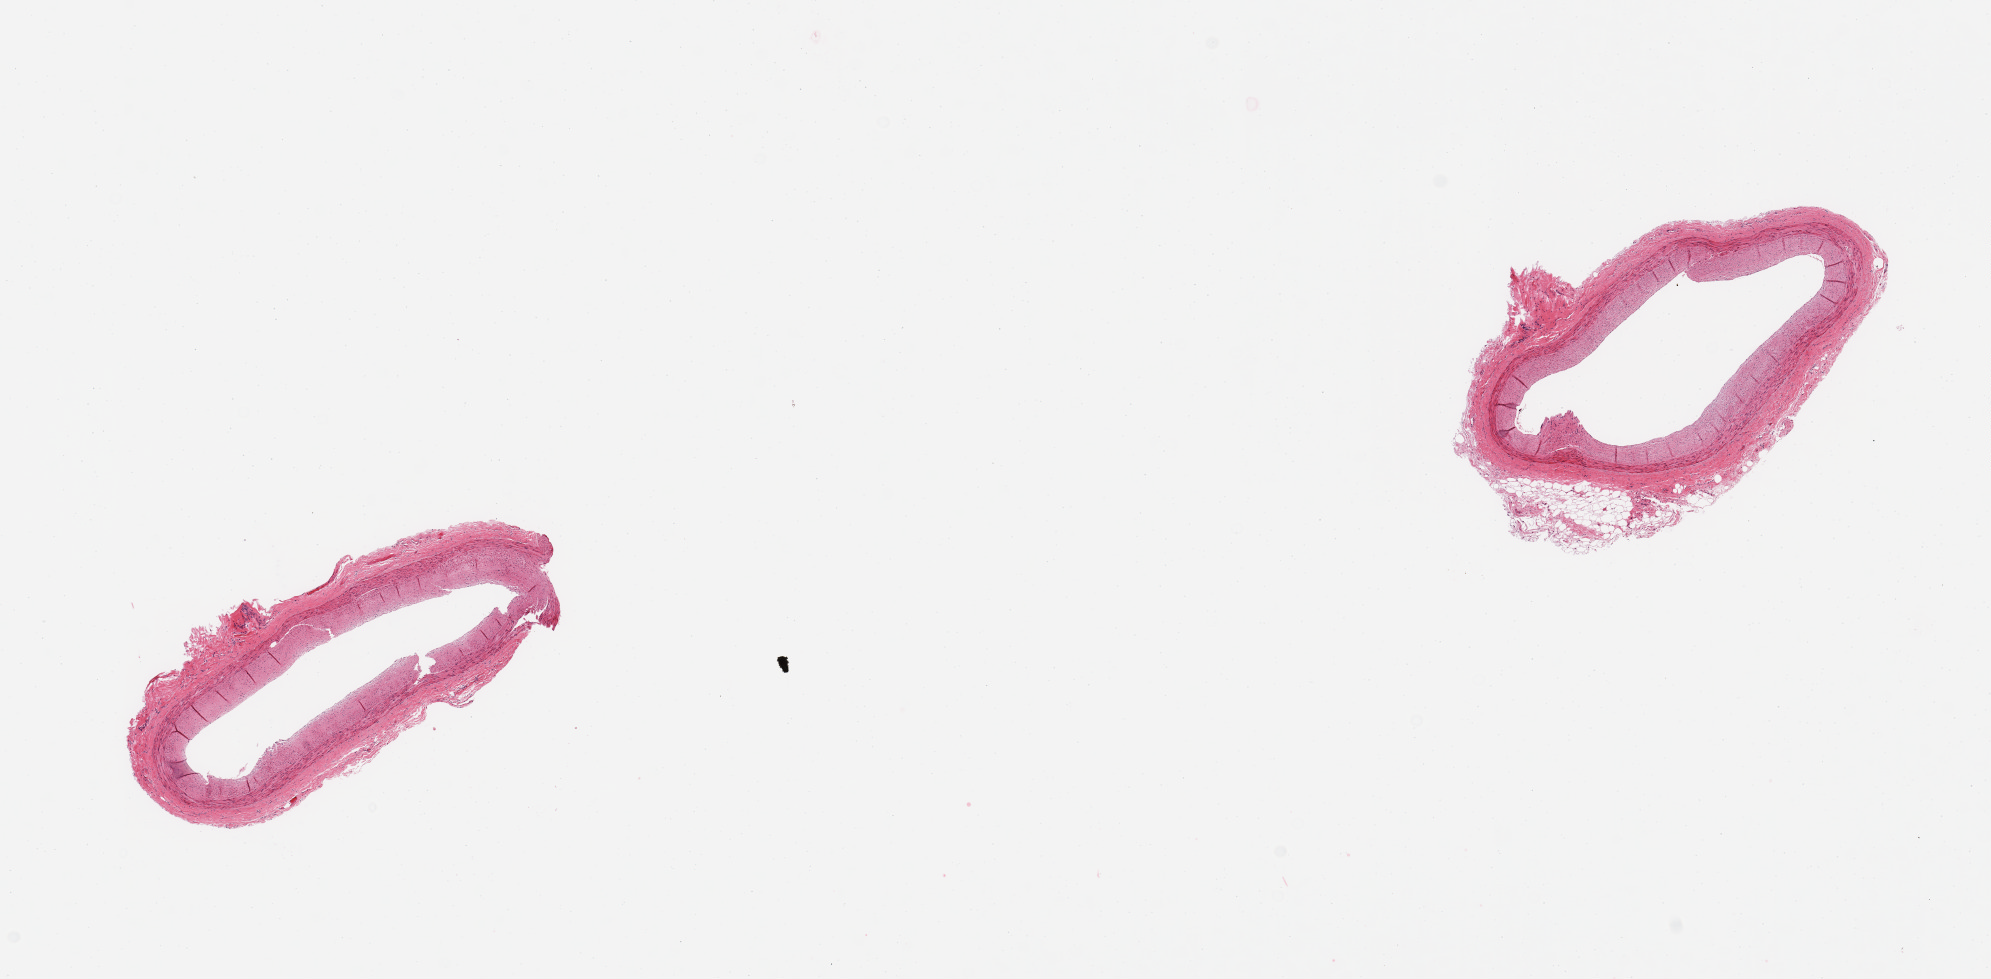
Haematoxylin and eosin whole-slide image — low-resolution overview of the scanned area, about 15.8 x 7.7 mm. PAXgene-fixed paraffin-embedded (PFPE) section. Sampled site (target tissue): coronary artery. Donor tissue sample.
Reviewer comment on this tissue sample: 2 pieces; linear fibrous plaques without luminal narrowing; well trimmed.